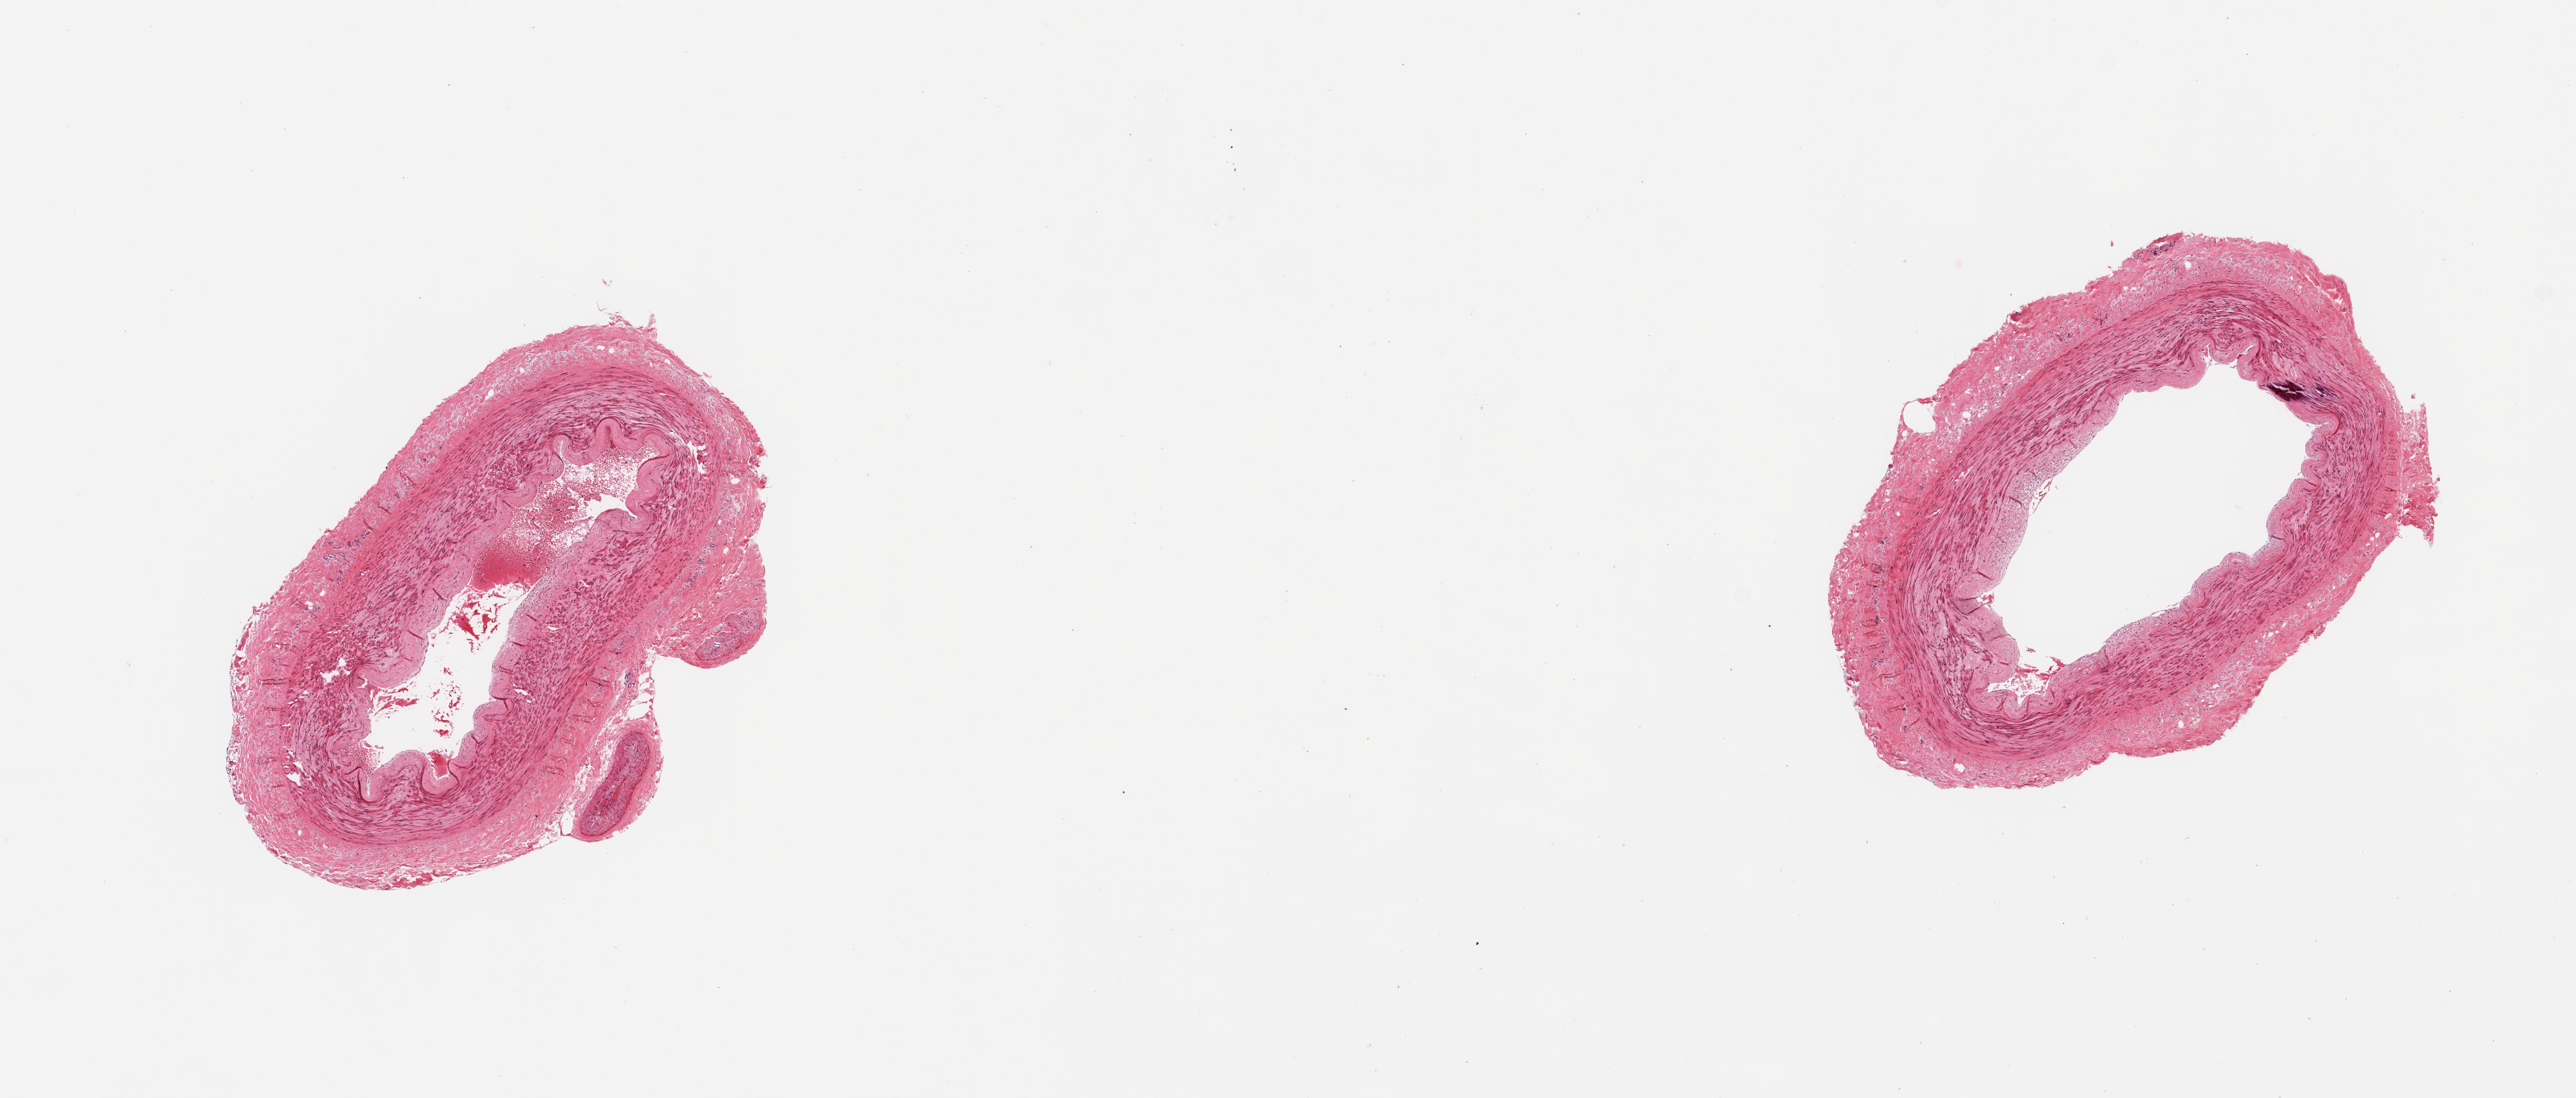
Whole-slide image, hematoxylin and eosin (H&E) stain — low-resolution overview of the scanned area, about 13.8 x 5.9 mm (from a 20x scan). PAXgene-fixed paraffin-embedded (PFPE) section. Sampled site (target tissue): tibial artery. Tissue donor sample. Male donor.
• reviewer comment on this tissue sample: 2 pieces; focal medial calcification and evolving plaque; up to 5mm adventitia